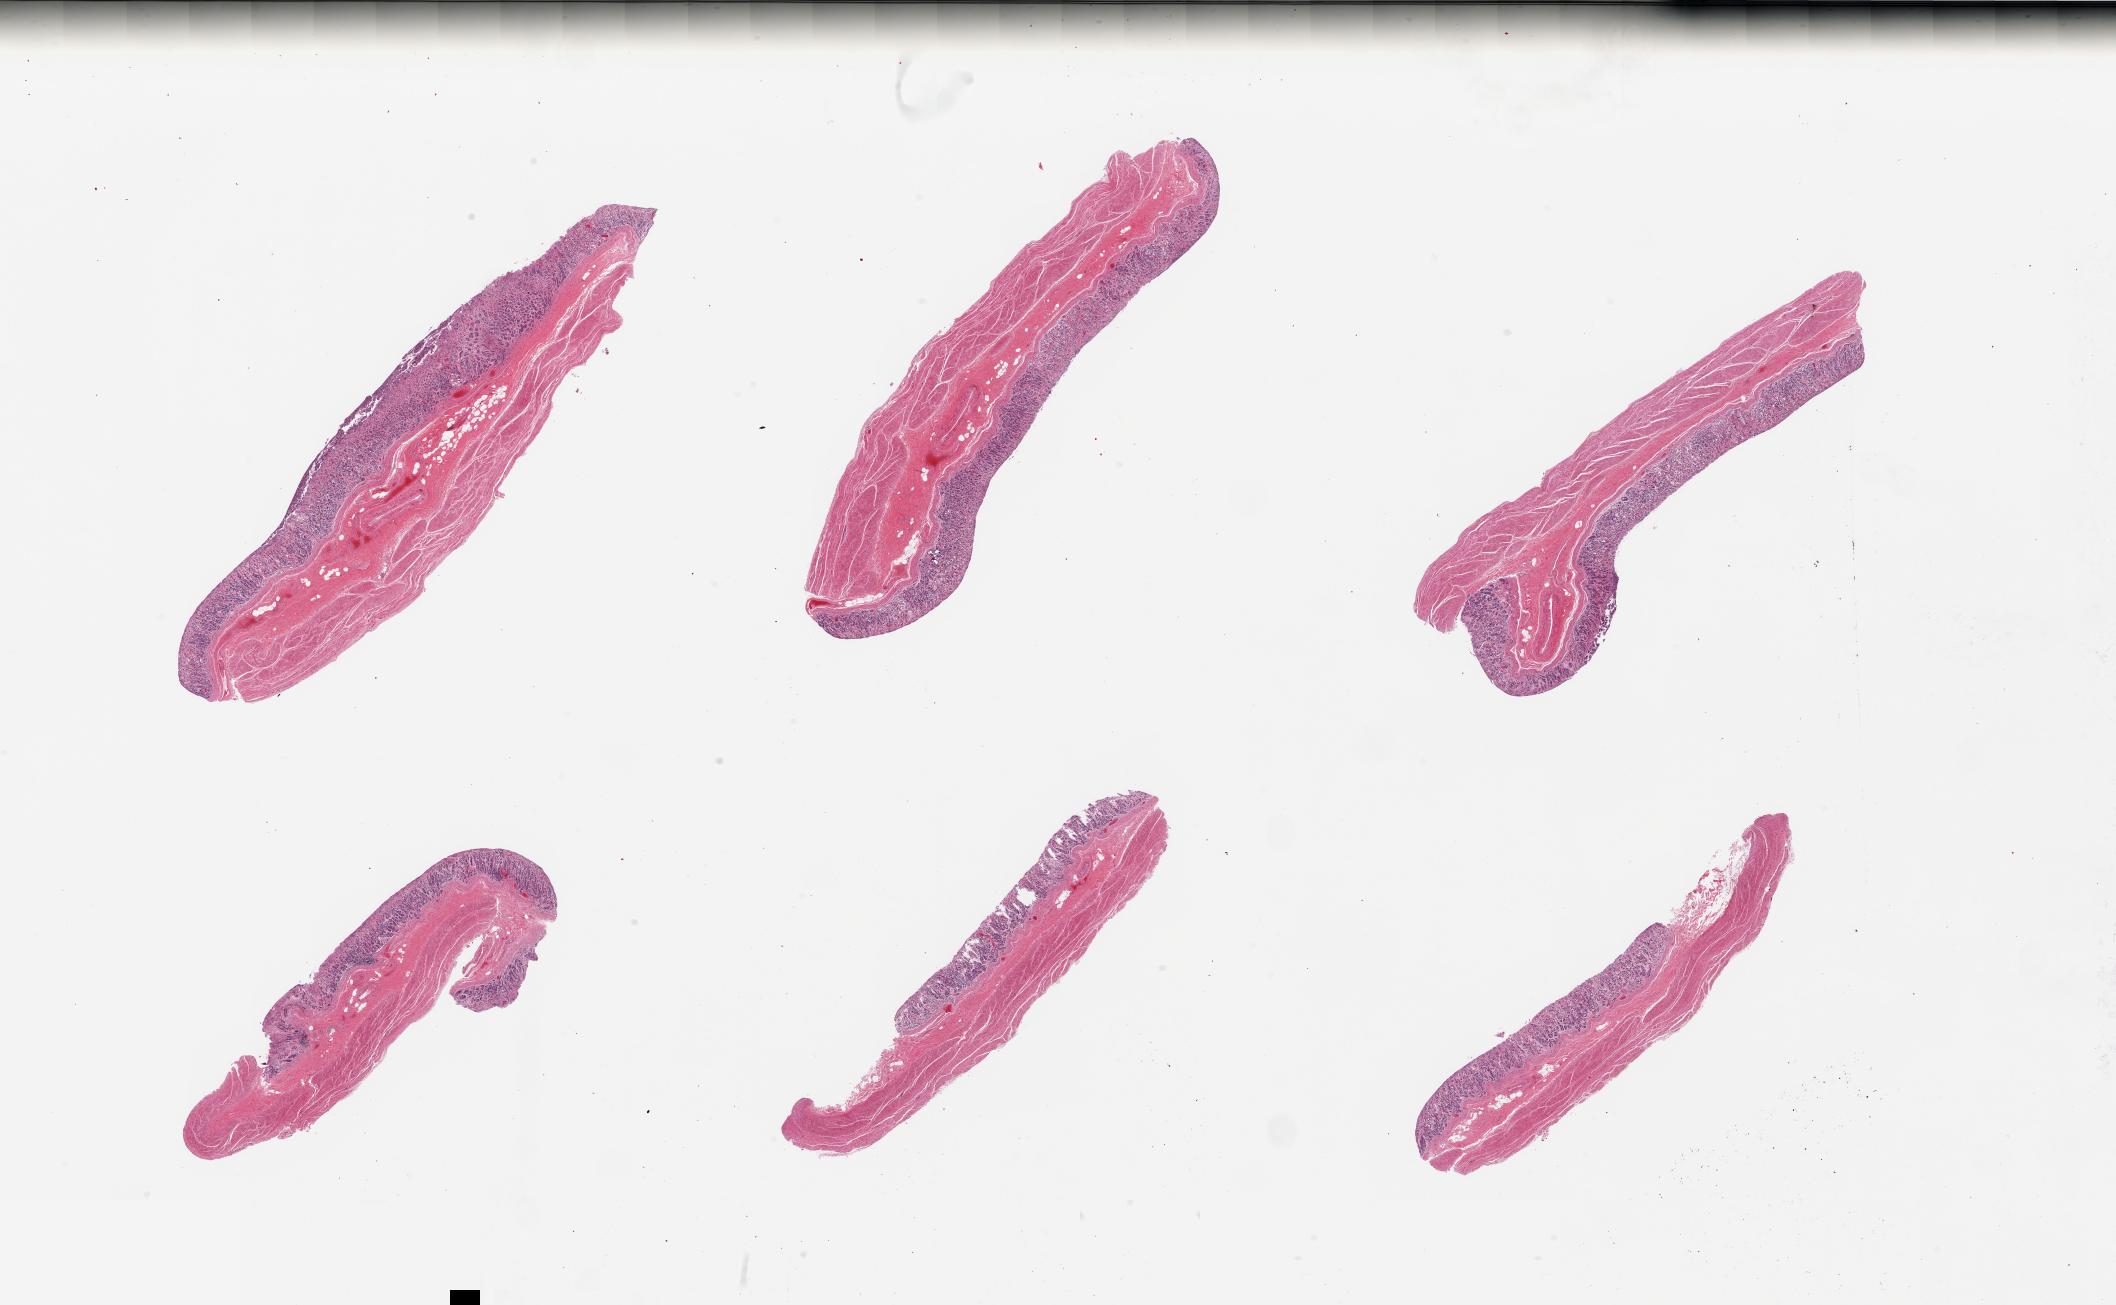
Digitized haematoxylin and eosin-stained section, shown as a low-resolution overview of the whole scanned area (about 33.5 x 20.6 mm). PAXgene-fixed paraffin-embedded (PFPE) section. Target tissue: stomach. Donor tissue sample. Donor: female.
Review note (as recorded): 6 pieces; full thickness sections, mucosa up to 0.6mm, superficial mucosal autolysis.